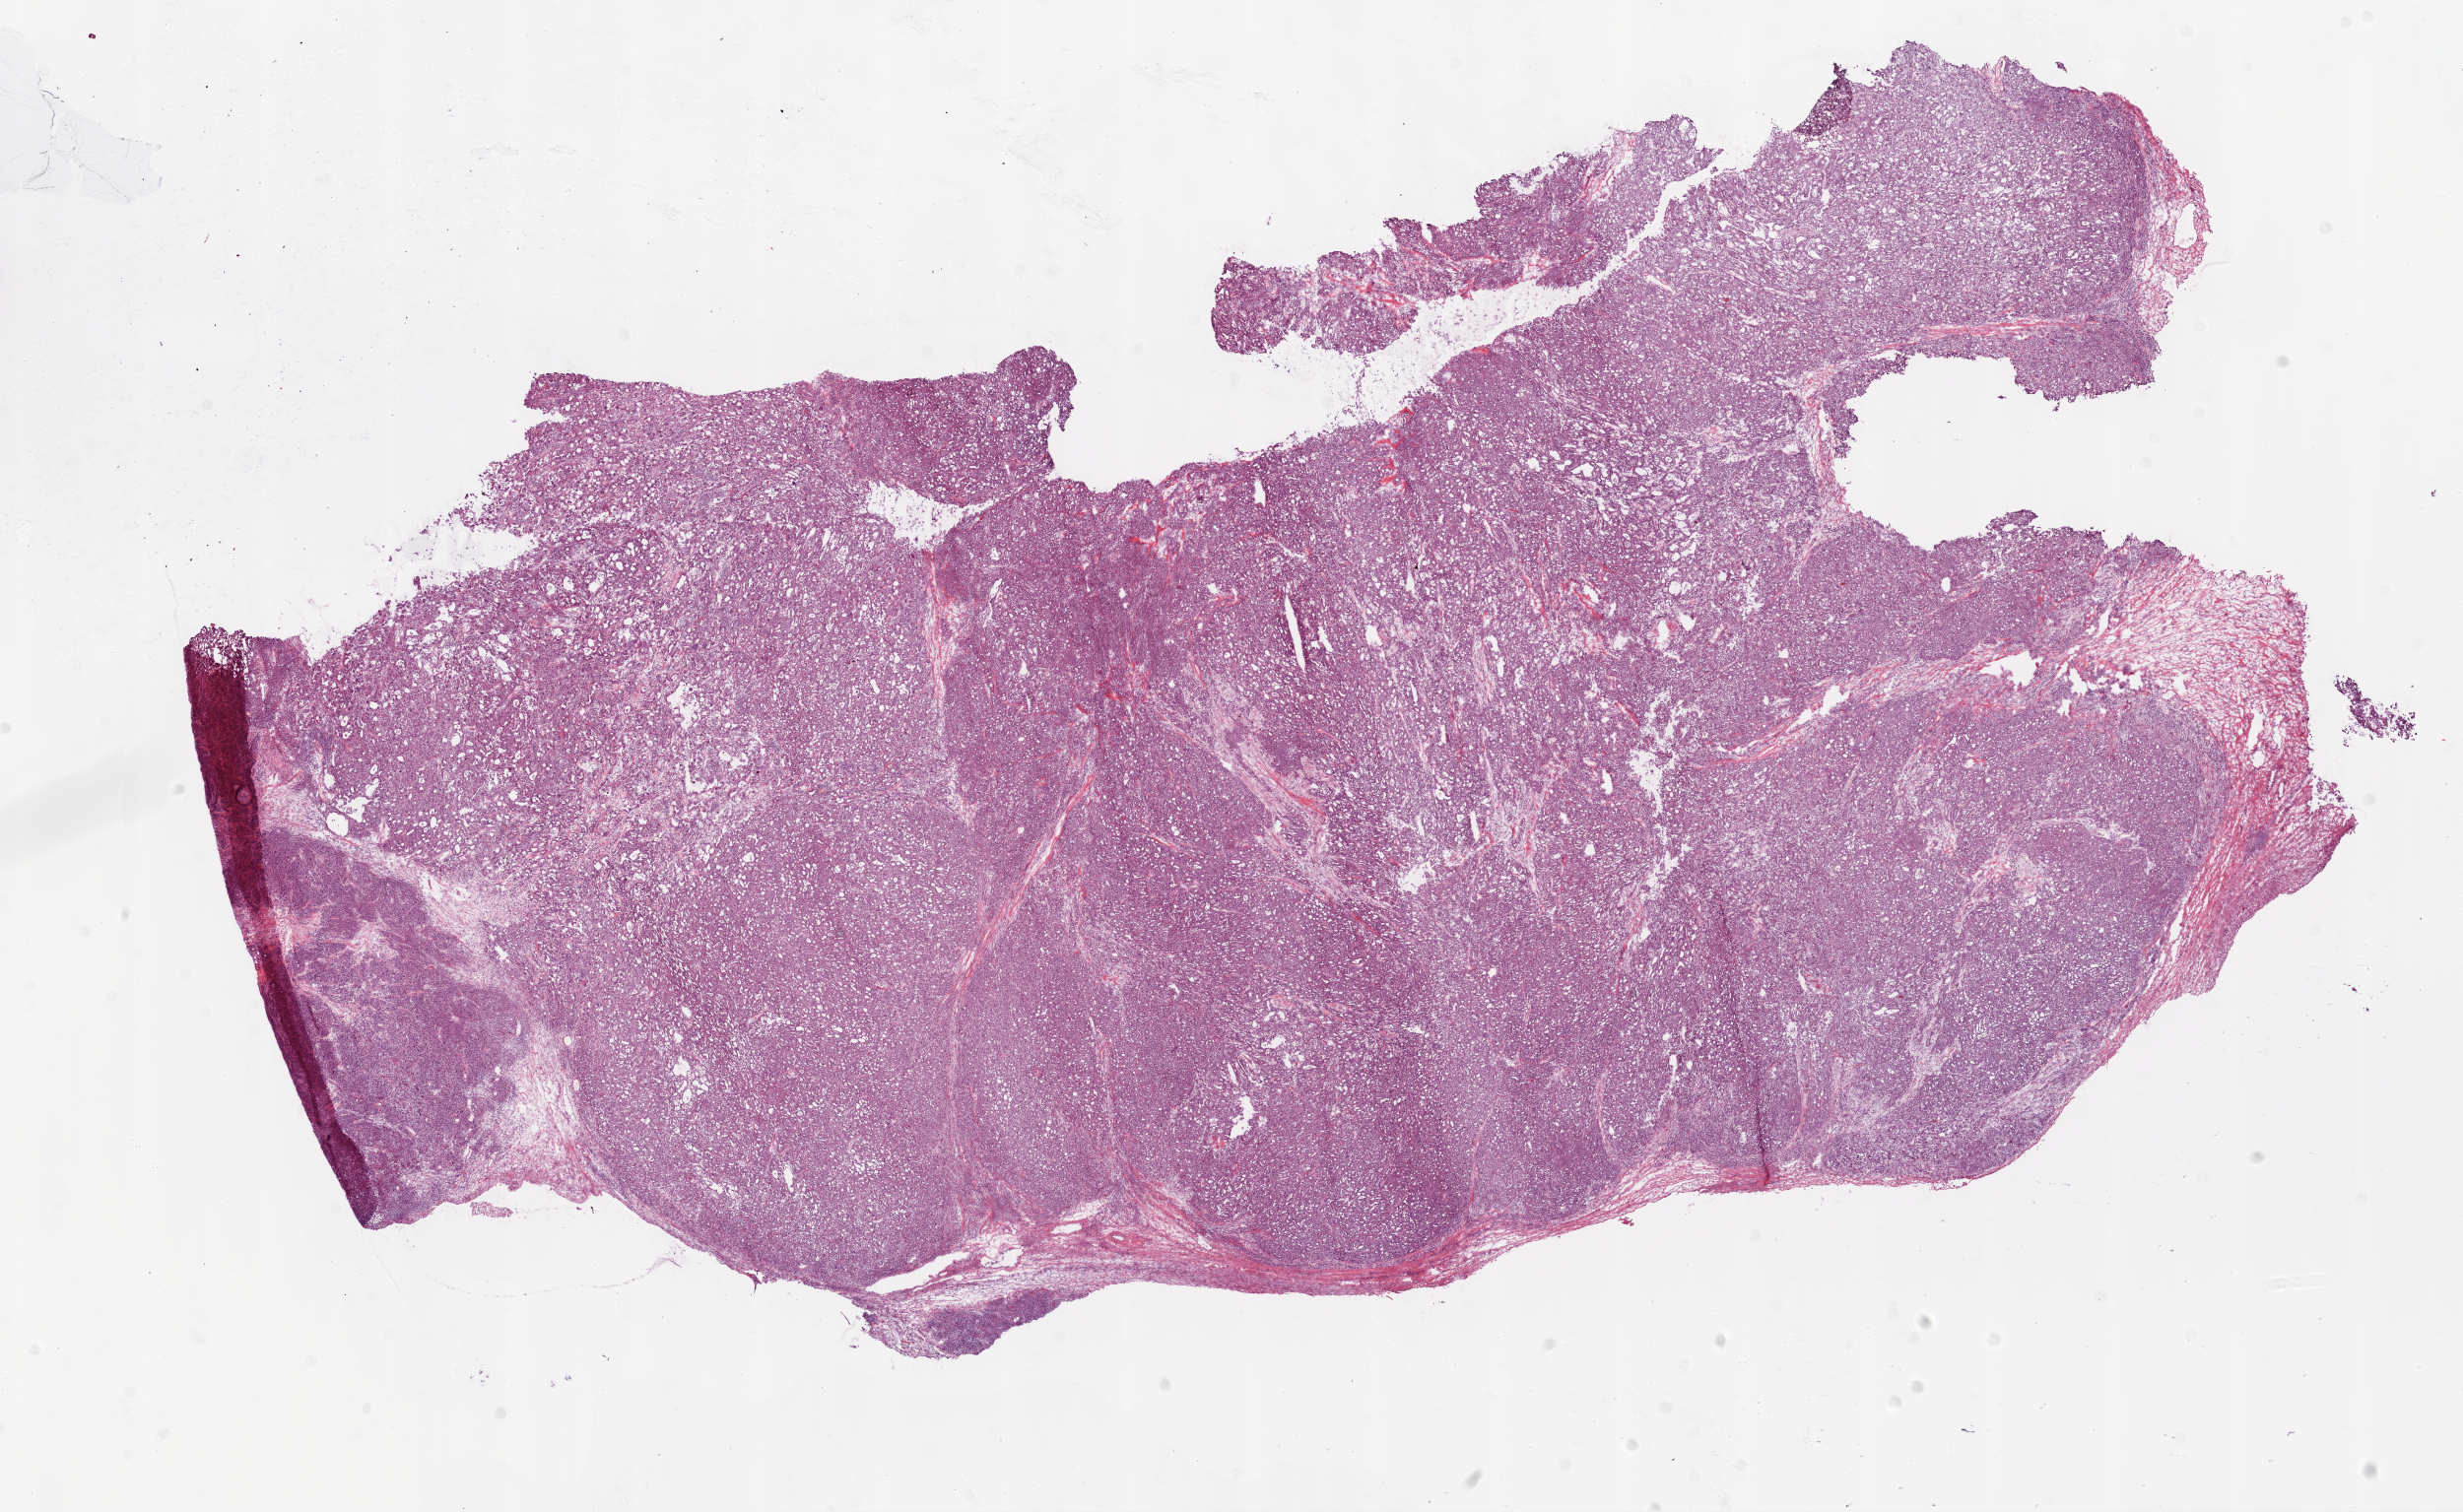
Digitized H&E tissue section (whole slide) — shown as a low-resolution overview of the whole scanned area (about 20.1 x 12.3 mm, acquisition: 20x scan); frozen section; primary tumour sample from the ovary. Female, age 55 years at initial diagnosis. Histologic grade: G3 (poorly differentiated). Composition of this section per pathologist review: tumour cells 95%, tumour nuclei 95%, normal cells 0%, stromal cells 5%, necrosis 0%.
- FIGO stage: IIA
- histologic diagnosis: Serous cystadenocarcinoma, NOS
- laterality: left